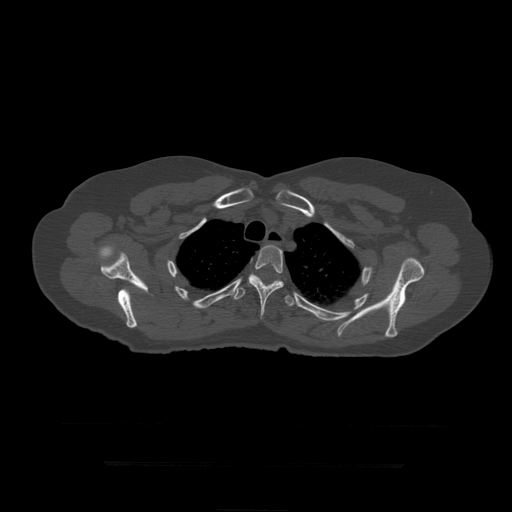
CT including the spine, one axial slice; position 347 of 399 along the scan axis; reconstruction kernel STANDARD; bone window (W 1800 / L 400 HU); 1.25 mm slice thickness; 512 × 512 image matrix, field of view 450 × 450 mm. Patient age 41 years. From the clinical record (not read from this slice): primary cancer: breast.
Annotated regions visible in this slice (semi-automatically segmented with operator editing):
- T4 vertebra: bounding box <248,245,284,319> (left, top, right, bottom; pixels)
- T5 vertebra: <233,274,296,307>